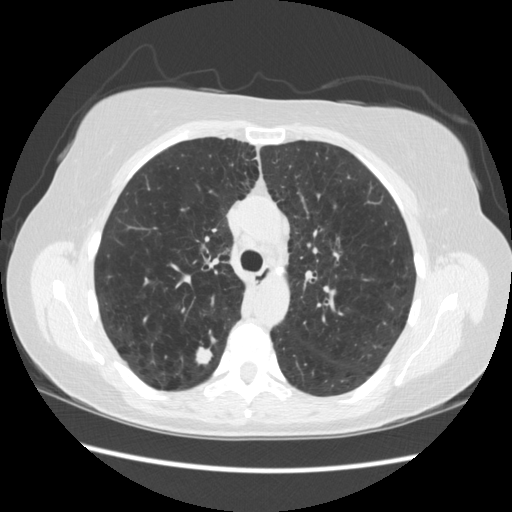
Low-dose screening chest CT, axial slice; third annual screen; lung window (W 1500 / L -600 HU); 2.5 mm slice thickness; slice 75 of 235 in the series. Female, age 55 years at enrolment. Current smoker at enrolment.
Expert-annotated lung lesion, bounding box (x1, y1, x2, y2) in pixels: (180, 331, 228, 375). Reader record for this screening exam (exam-level; its link to the box is not recorded): non-calcified nodule or mass ≥4 mm, right upper lobe, 11 × 11 mm, poorly defined margins, soft tissue attenuation, pre-existing on the prior screen: no. Later outcome: lung cancer diagnosed 96 days after this screen — small cell carcinoma, NOS, right upper lobe.